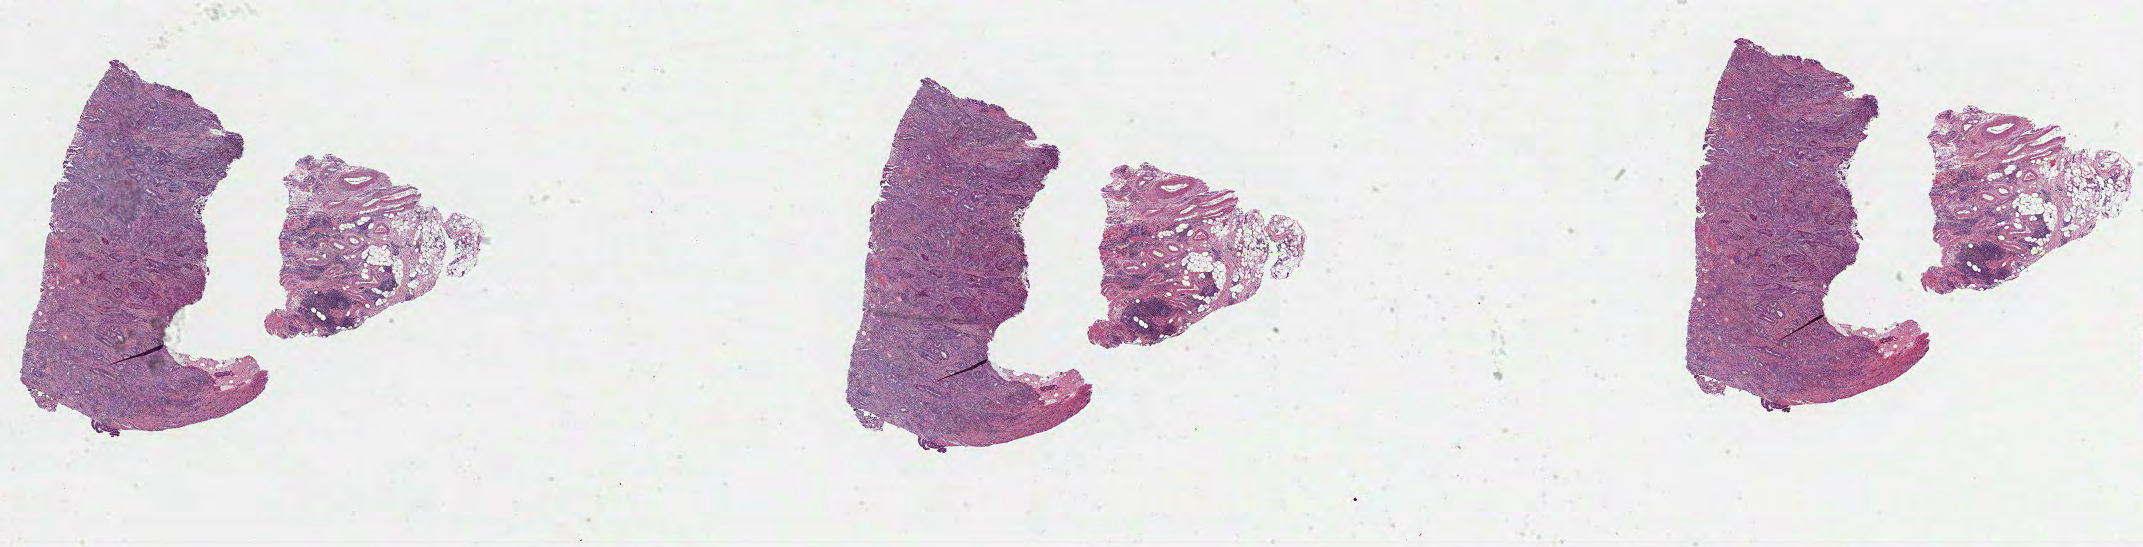
Digitized H&E-stained tissue section (whole slide), a low-resolution overview of the entire scanned area, about 34.6 x 8.8 mm (acquisition: 40x scan); formalin-fixed paraffin-embedded (FFPE) diagnostic section; colon, primary tumour sample. Male, age 61 years at initial diagnosis.
- AJCC pathologic stage: I
- histologic diagnosis: Adenocarcinoma, NOS (cecum)
- lymph nodes positive (case pathology): 0 of 24 examined
- TNM: T2 N0 M0